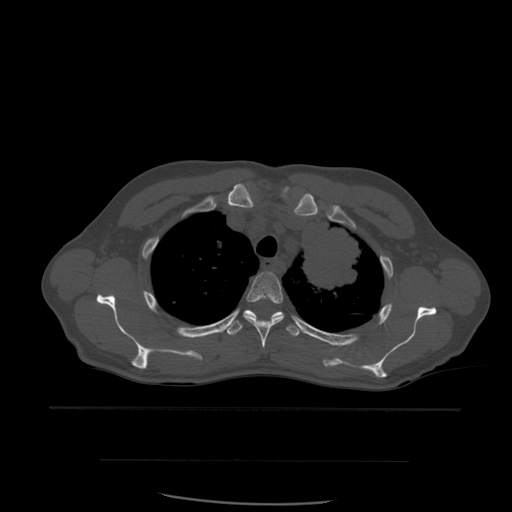
CT including the spine, one axial slice. Slice 438 of 574 in the series (ordered by position). Bone window (W 1800 / L 400 HU). 1.25 mm slice thickness. 512 × 512 image matrix, field of view 392 × 392 mm. Patient age 48 years. From the clinical record (not read from this slice): primary cancer: lung; vertebrae with lytic lesions (as recorded): T11.
Outlined on this slice (semi-automatically segmented with operator editing):
- T3 vertebra: bounding box <243,272,284,349> (left, top, right, bottom; pixels)
- T4 vertebra: <224,310,302,337>